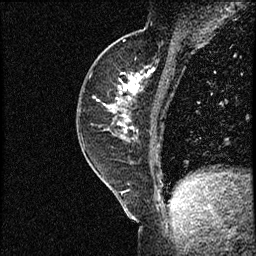
Breast MRI (dynamic contrast-enhanced), one sagittal slice. Slice 29 of 56 in the series (ordered by position). Dynamic contrast-enhanced study with each time point stored as its own series, time point 2 of 3 at this slice position (early post-contrast, ordered by acquisition time). 1.5 T. TE 4.2 ms, TR 17.3 ms. 256 × 256 image matrix. Female patient. Case-level facts recorded for this patient, not image findings: setting: breast cancer imaged before/during neoadjuvant chemotherapy; receptor status: HER2-positive.
Outlined on this slice (semi-automatically segmented with operator editing):
- analysis volume of interest (the breast-tissue region the enhancement analysis was run in; not a lesion): bounding box (x1, y1, x2, y2) in pixels: (77, 50, 156, 155)
- tumour enhancement mask (voxels above the 100 % enhancement threshold inside the analysis volume of interest): (103, 69, 154, 132)